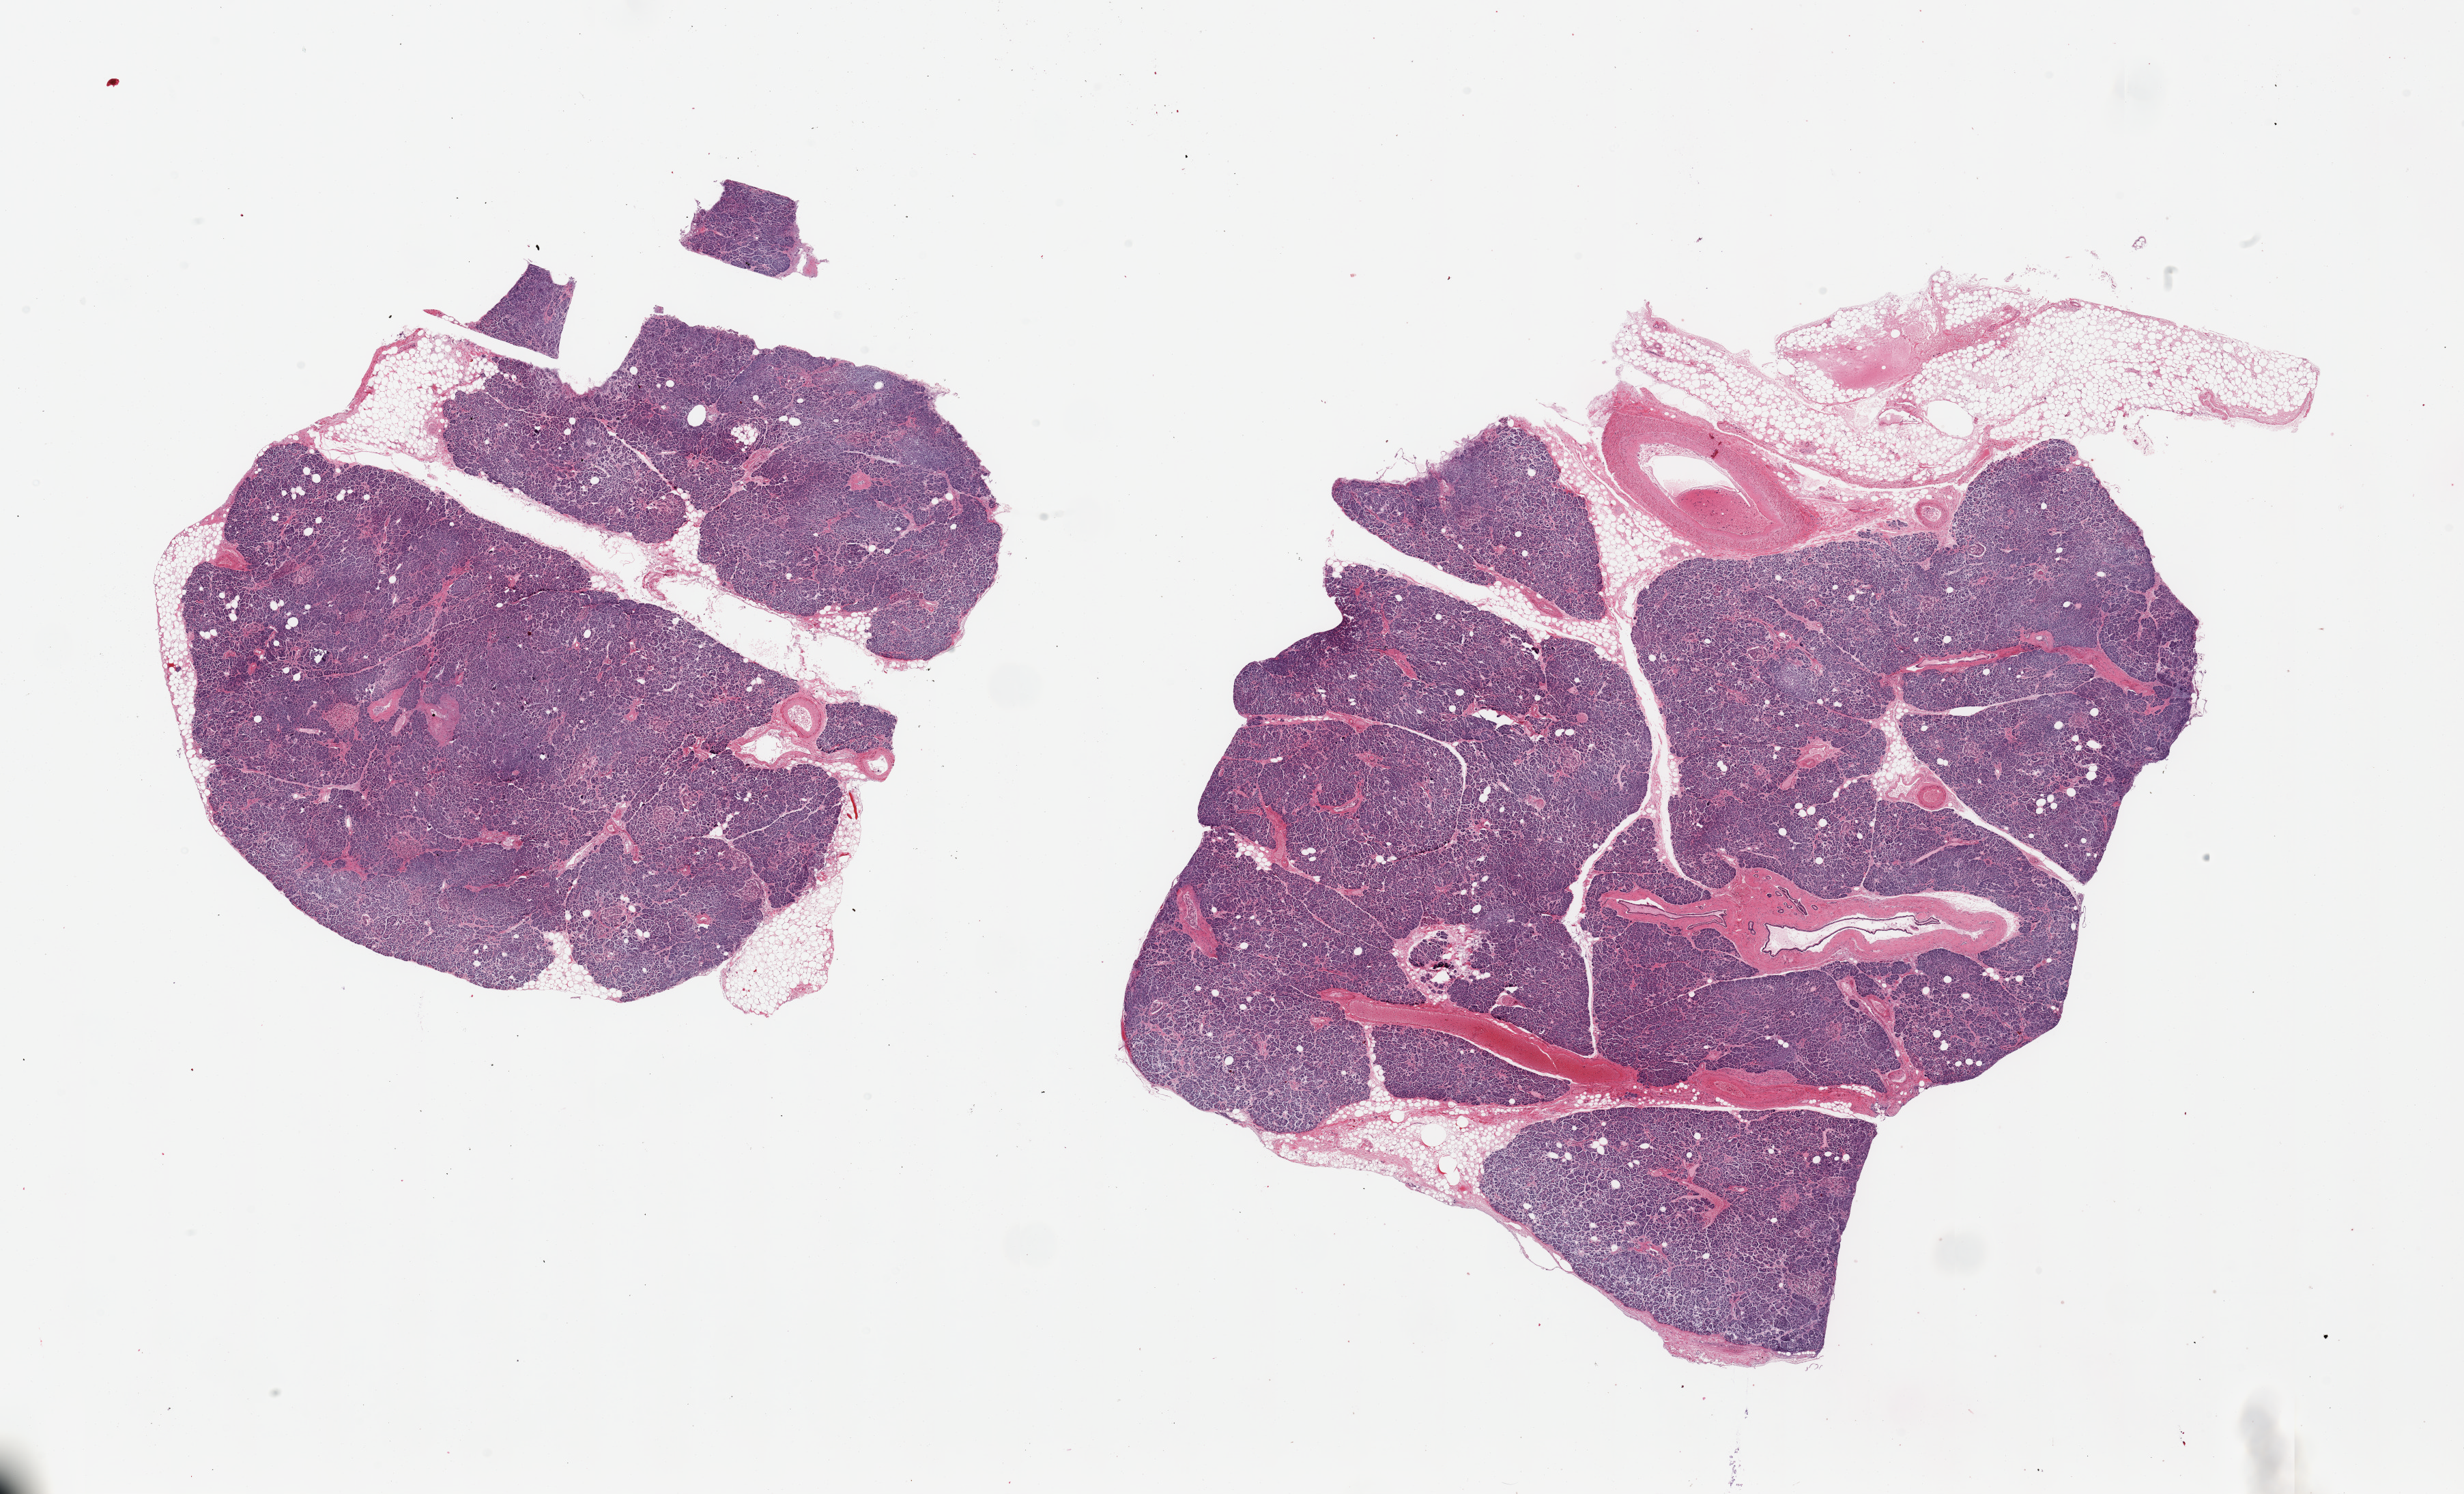
Whole-slide image, H&E stain, low-resolution overview of the scanned area, about 28.5 x 17.3 mm (slide scanned at 20x), PAXgene-fixed paraffin-embedded (PFPE) section, section of pancreas (target tissue), donor tissue sample.
Review note (as recorded): 2 pieces; includes ~10% fat and larger vessel, interstitial fibrosis.